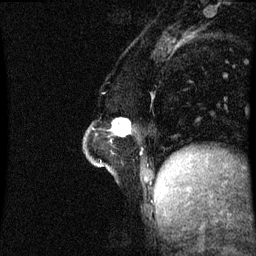
Breast MRI (dynamic contrast-enhanced), one sagittal slice. Slice 18 of 60 in the series (ordered by position). Dynamic contrast-enhanced series, image 2 of 3 at this slice position (ordered by acquisition). 1.5 T. TE 4.2 ms, TR 8.9 ms. 2.1 mm slice thickness. 256 × 256 image matrix, field of view 200 × 200 mm. Female patient, age 47 years. Case-level facts recorded for this patient, not image findings: setting: breast cancer imaged before/during neoadjuvant chemotherapy; receptor status: HR-positive, HER2-negative.
Structures marked on this image (semi-automatically segmented with operator editing):
- analysis volume of interest (the breast-tissue region the enhancement analysis was run in; not a lesion): bounding box <85,120,132,163> (left, top, right, bottom; pixels)
- tumour enhancement mask (voxels above the 70 % enhancement threshold inside the analysis volume of interest): <114,120,131,137>